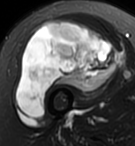
MRI of an extremity soft-tissue mass, one axial slice; slice 57 of 95 in the series (ordered by position); T2-weighted fat-saturated; MR volume resampled by the dataset authors to the PET/CT grid (not the native acquisition matrix); 135 × 146 image matrix, field of view 132 × 143 mm. Female patient. Case-level facts recorded for this patient, not image findings: histological type: pleiomorphic undifferentiated sarcoma; grade: high; site of the primary tumour: right quadricep.
Outlined on this slice (expert contour drawn on MRI and transferred to this co-registered scan by the dataset authors):
- gross tumour volume including surrounding oedema: bounding box [x1, y1, x2, y2] px = [16, 20, 122, 119]
- gross tumour volume (mass): [16, 20, 122, 119]